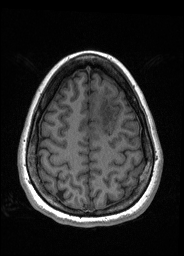
Pre-operative brain MRI before brain-tumour surgery, one axial slice; position 52 of 176 along the scan axis; T1-weighted post-contrast; 1 mm slice thickness; 184 × 256 image matrix, field of view 180 × 250 mm. Case-level facts recorded for this patient, not image findings: histopathology: Oligodendroglioma; WHO grade: 2; IDH mutation: yes; tumour location: Left Frontal.
Annotated regions visible in this slice (outlined manually by an expert reader):
- tumour: bounding box <91,96,117,135> (left, top, right, bottom; pixels)